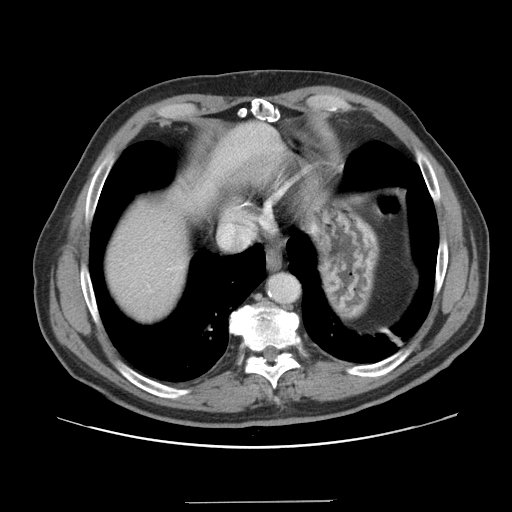
Contrast-enhanced abdominal CT, one axial slice. Slice 140 of 151 in the series (ordered by position). 120 kVp. Intravenous contrast given. Soft-tissue window (W 400 / L 40 HU). 512 × 512 image matrix, field of view 399 × 399 mm. Male patient, age 63 years. Case-level facts recorded for this patient, not image findings: diagnosis: colorectal cancer liver metastases, imaged before liver resection; multiple liver metastases: no; largest metastasis: 2.1 cm; disease in both lobes: no.
Structures marked on this image (manually delineated by an expert):
- hepatic veins: bounding box (x1, y1, x2, y2) in pixels: (222, 226, 249, 243)
- liver: (102, 122, 287, 325)
- planned liver remnant (the part of the liver to remain after resection): (102, 167, 220, 326)